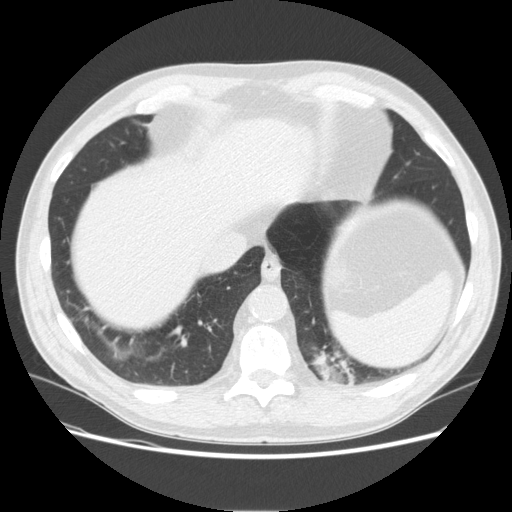
Low-dose screening chest CT, one axial slice. Slice 48 of 165 in the series (ordered by position). Reconstruction kernel STANDARD. 120 kVp. Lung window (W 1500 / L -600 HU). 2.5 mm slice thickness. 512 × 512 image matrix, field of view 375 × 375 mm.
Structures marked on this image (outlined manually by an expert reader):
- lesion 1 (tumor, upper lobe of left lung): bounding box [x1, y1, x2, y2] px = [311, 351, 356, 385]